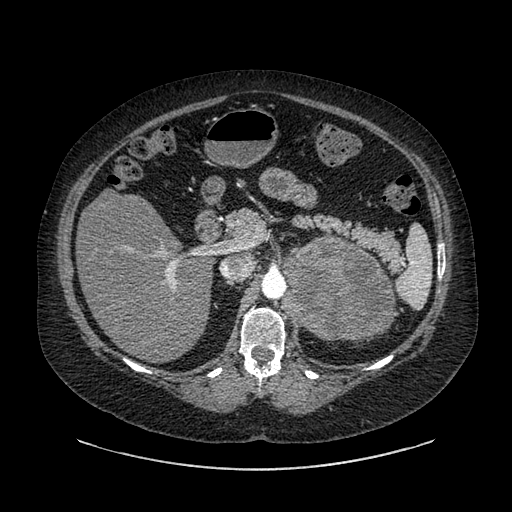
Contrast-enhanced abdominal CT, one axial slice; slice 569 of 769 in the series (ordered by position); intravenous contrast given; soft-tissue window (W 400 / L 40 HU); 0.62 mm slice thickness; 512 × 512 image matrix, field of view 460 × 460 mm. Female patient, age 61 years. Case-level facts recorded for this patient, not image findings: diagnosis: adrenocortical carcinoma; tumour side: left adrenal; tumour size at pathology: 13 cm; Ki-67 index: 79 %; stage (as recorded): 2.
Outlined on this slice (semi-automatic segmentation, software-assisted and operator-edited):
- mass: bounding box [x1, y1, x2, y2] px = [280, 236, 391, 340]